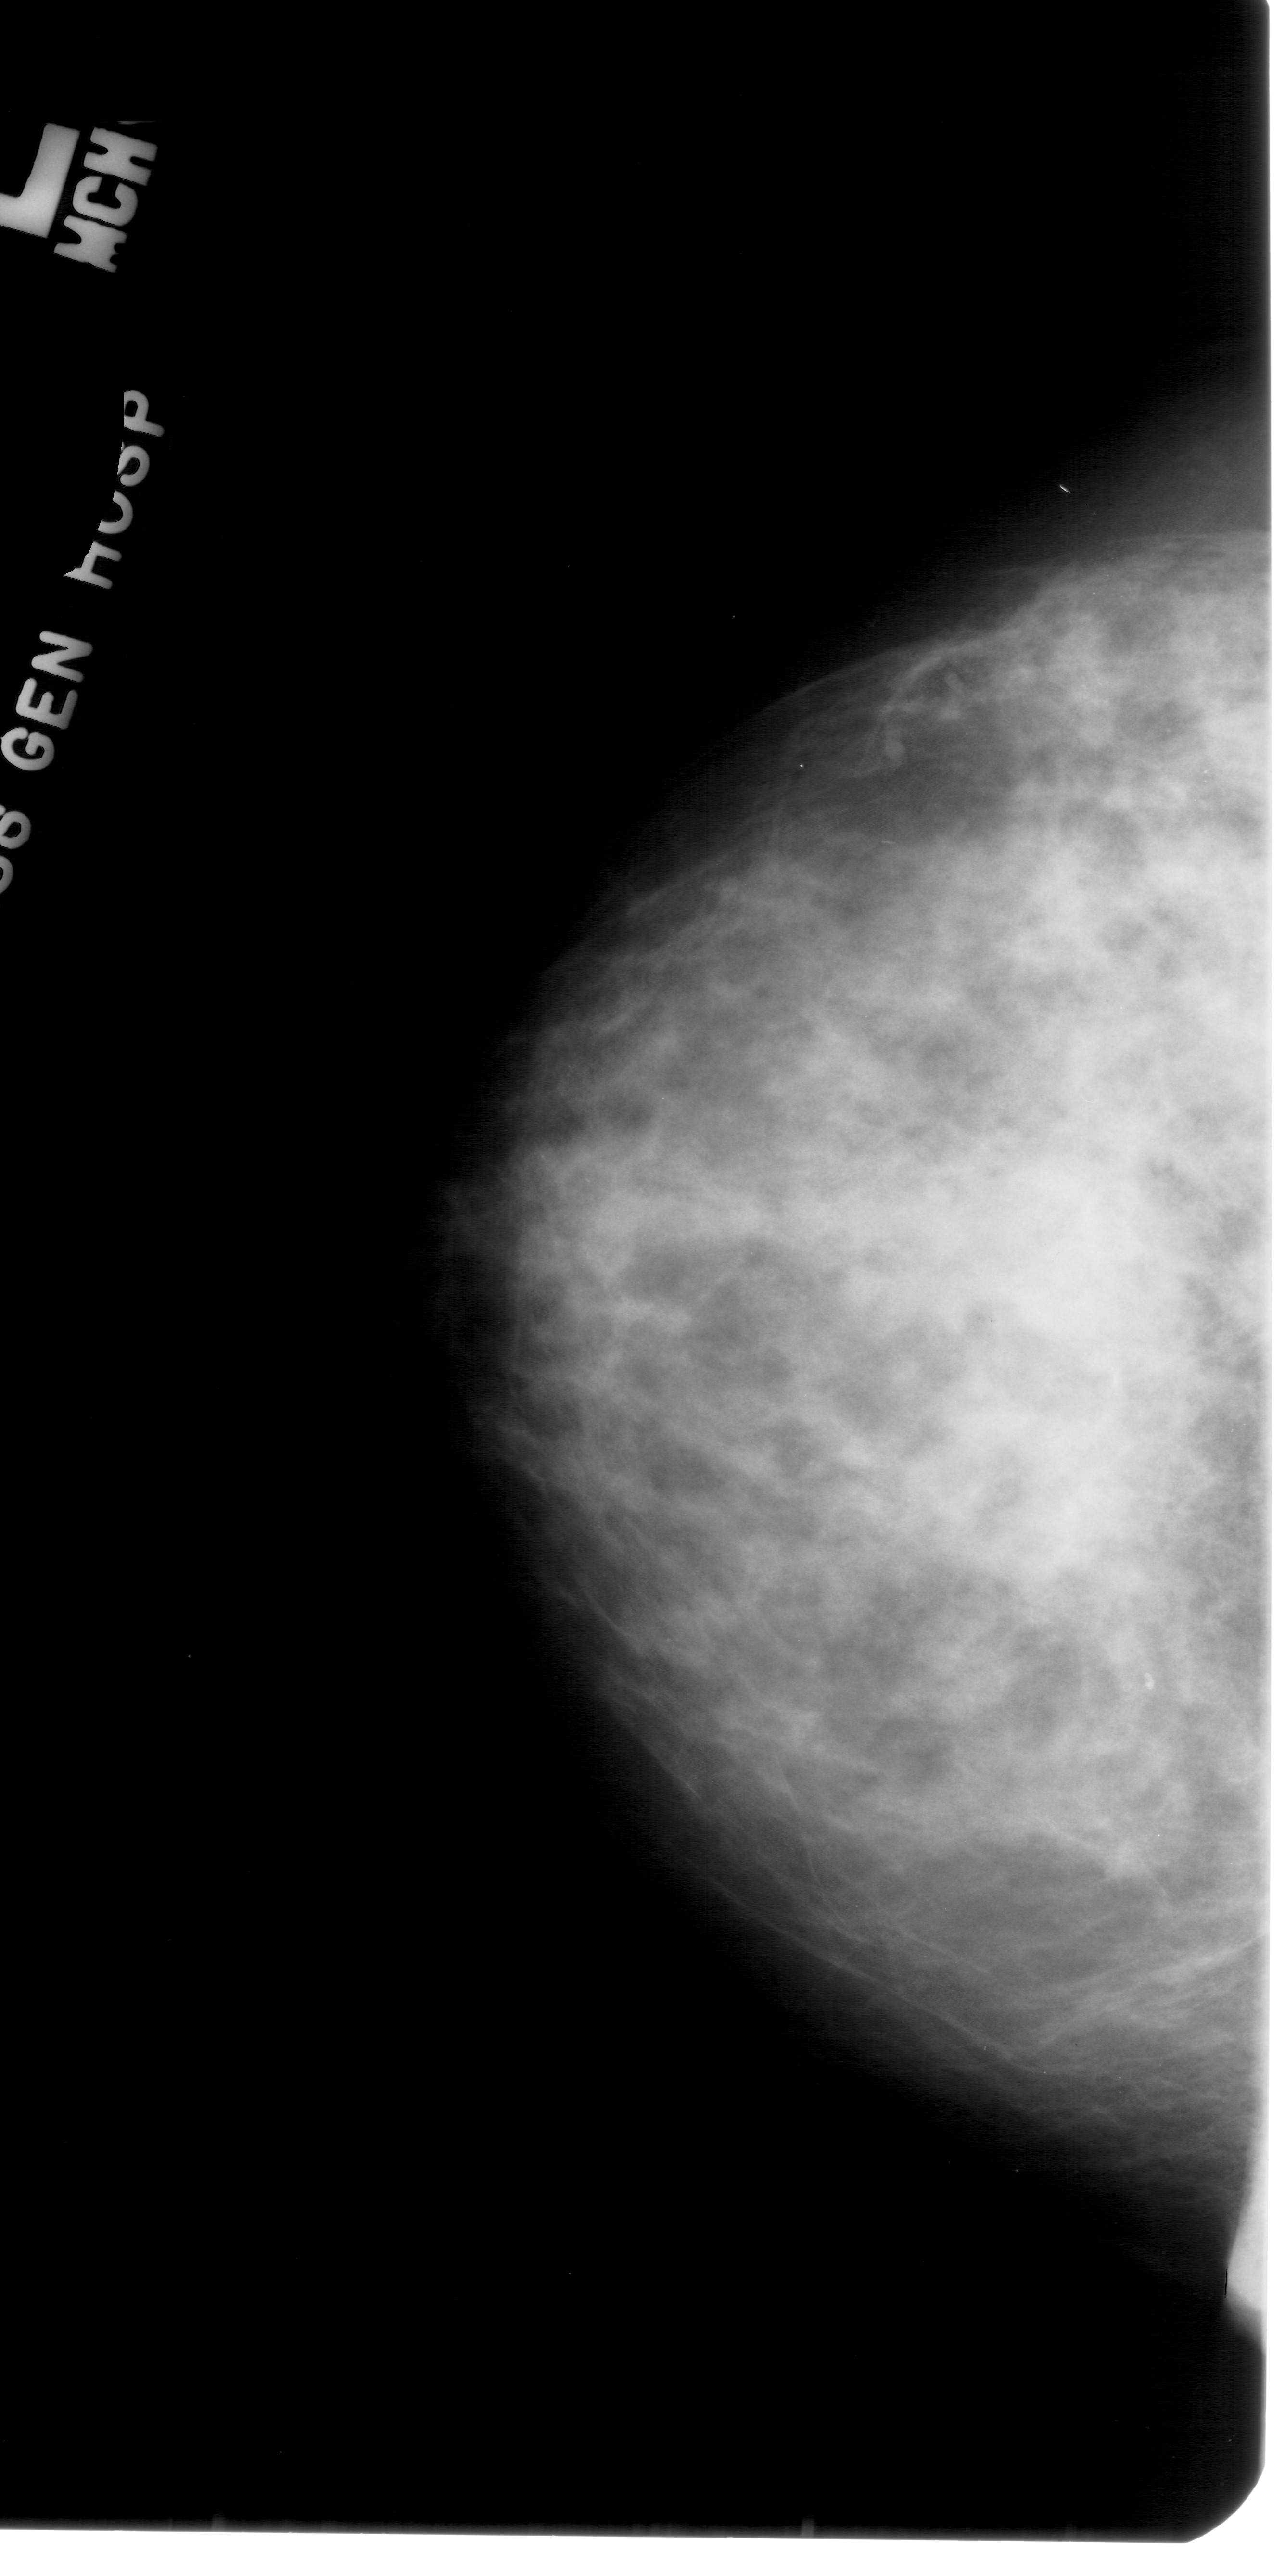
Scanned film-screen mammogram; left breast; craniocaudal (CC) view; breast composition: heterogeneously dense (BI-RADS density category 3 of 4); 1285 × 2576 image matrix.
Expert-marked regions of interest on this image (one box per marked abnormality):
- calcifications, morphology pleomorphic, distribution clustered; BI-RADS assessment category 4; pathology (as recorded): benign: bounding box [x1, y1, x2, y2] px = [983, 629, 1185, 754]